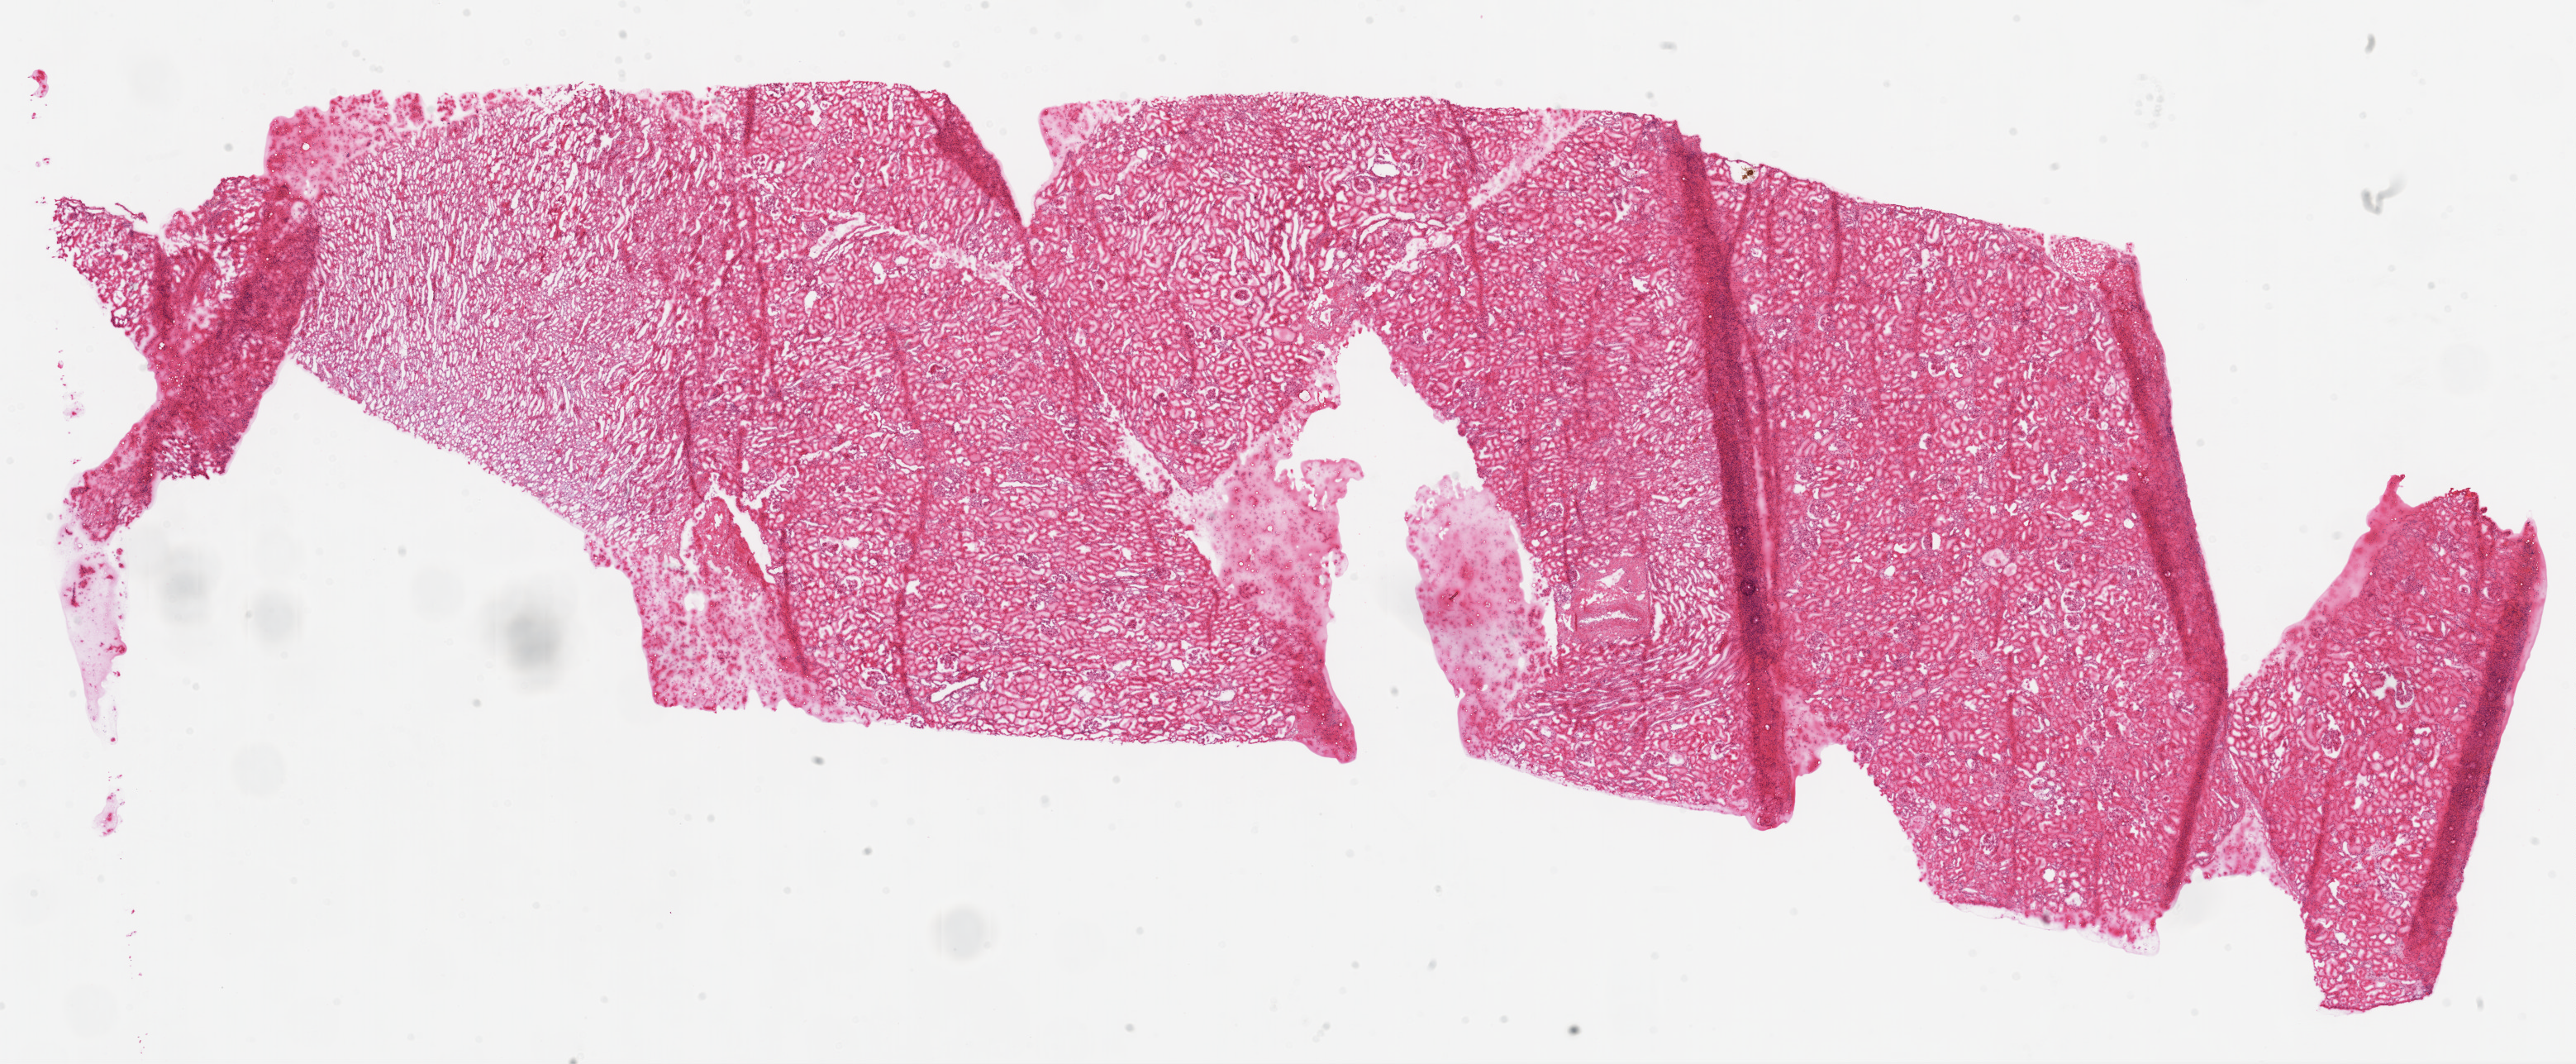
Whole-slide histology image, H&E-stained, low-resolution overview of the scanned area, about 25.1 x 10.4 mm (from a 20x scan). Frozen section from the top of the tissue portion. Solid tissue normal (non-tumour tissue) sample from the kidney. Male, age 70 years at initial diagnosis.
• this section: solid tissue normal sample (biorepository sample class)
• patient diagnosis: Clear cell adenocarcinoma, NOS